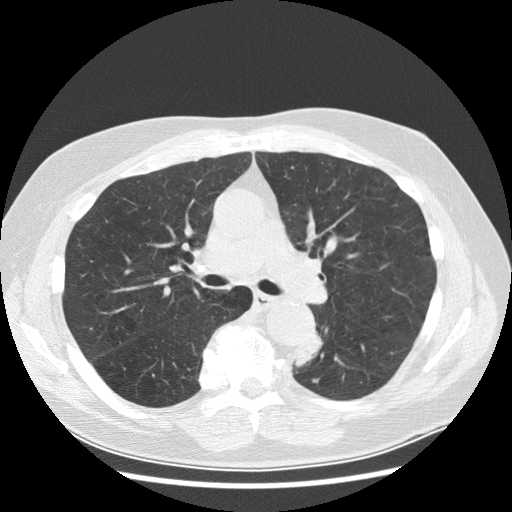
Low-dose screening chest CT, one axial slice. Position 175 of 282 along the scan axis. Reconstruction kernel STANDARD. 120 kVp. Lung window (W 1500 / L -600 HU). 512 × 512 image matrix, field of view 370 × 370 mm.
Structures marked on this image (manually delineated by an expert):
- lesion 1 (tumor, lower lobe of left lung): bounding box (x1, y1, x2, y2) in pixels: (292, 333, 323, 367)